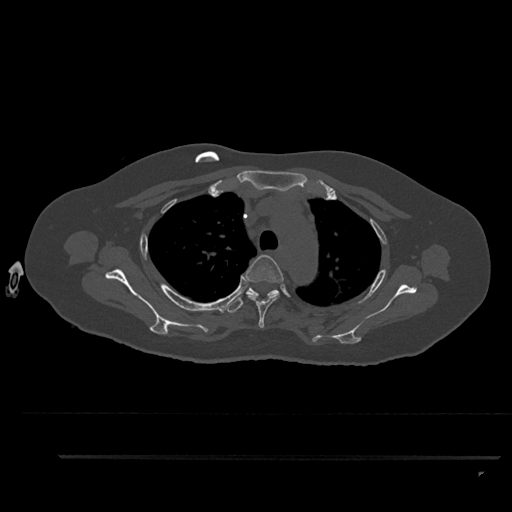
CT including the spine, one axial slice. Position 667 of 797 along the scan axis. Reconstruction kernel Br40s/3. Bone window (W 1800 / L 400 HU). 0.5 mm slice thickness. 512 × 512 image matrix, field of view 408 × 408 mm. Female patient, age 44 years. From the clinical record (not read from this slice): primary cancer: renal; vertebrae with lytic lesions (as recorded): L1.
Outlined on this slice (semi-automatically segmented with operator editing):
- T3 vertebra: bounding box [x1, y1, x2, y2] px = [241, 255, 284, 328]
- T4 vertebra: [227, 288, 279, 313]